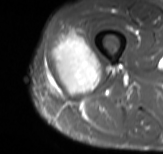
MRI of an extremity soft-tissue mass, one axial slice; position 30 of 61 along the scan axis; STIR; MR volume resampled by the dataset authors to the PET/CT grid (not the native acquisition matrix); 163 × 154 image matrix, field of view 159 × 150 mm. Male patient. From the clinical record (not read from this slice): histological type: poorly differentiated synovial sarcoma; grade: high; site of the primary tumour: right buttock.
Outlined on this slice (expert contour drawn on MRI and transferred to this co-registered scan by the dataset authors):
- gross tumour volume including surrounding oedema: bounding box [x1, y1, x2, y2] px = [50, 25, 101, 95]
- gross tumour volume (mass): [52, 34, 101, 95]